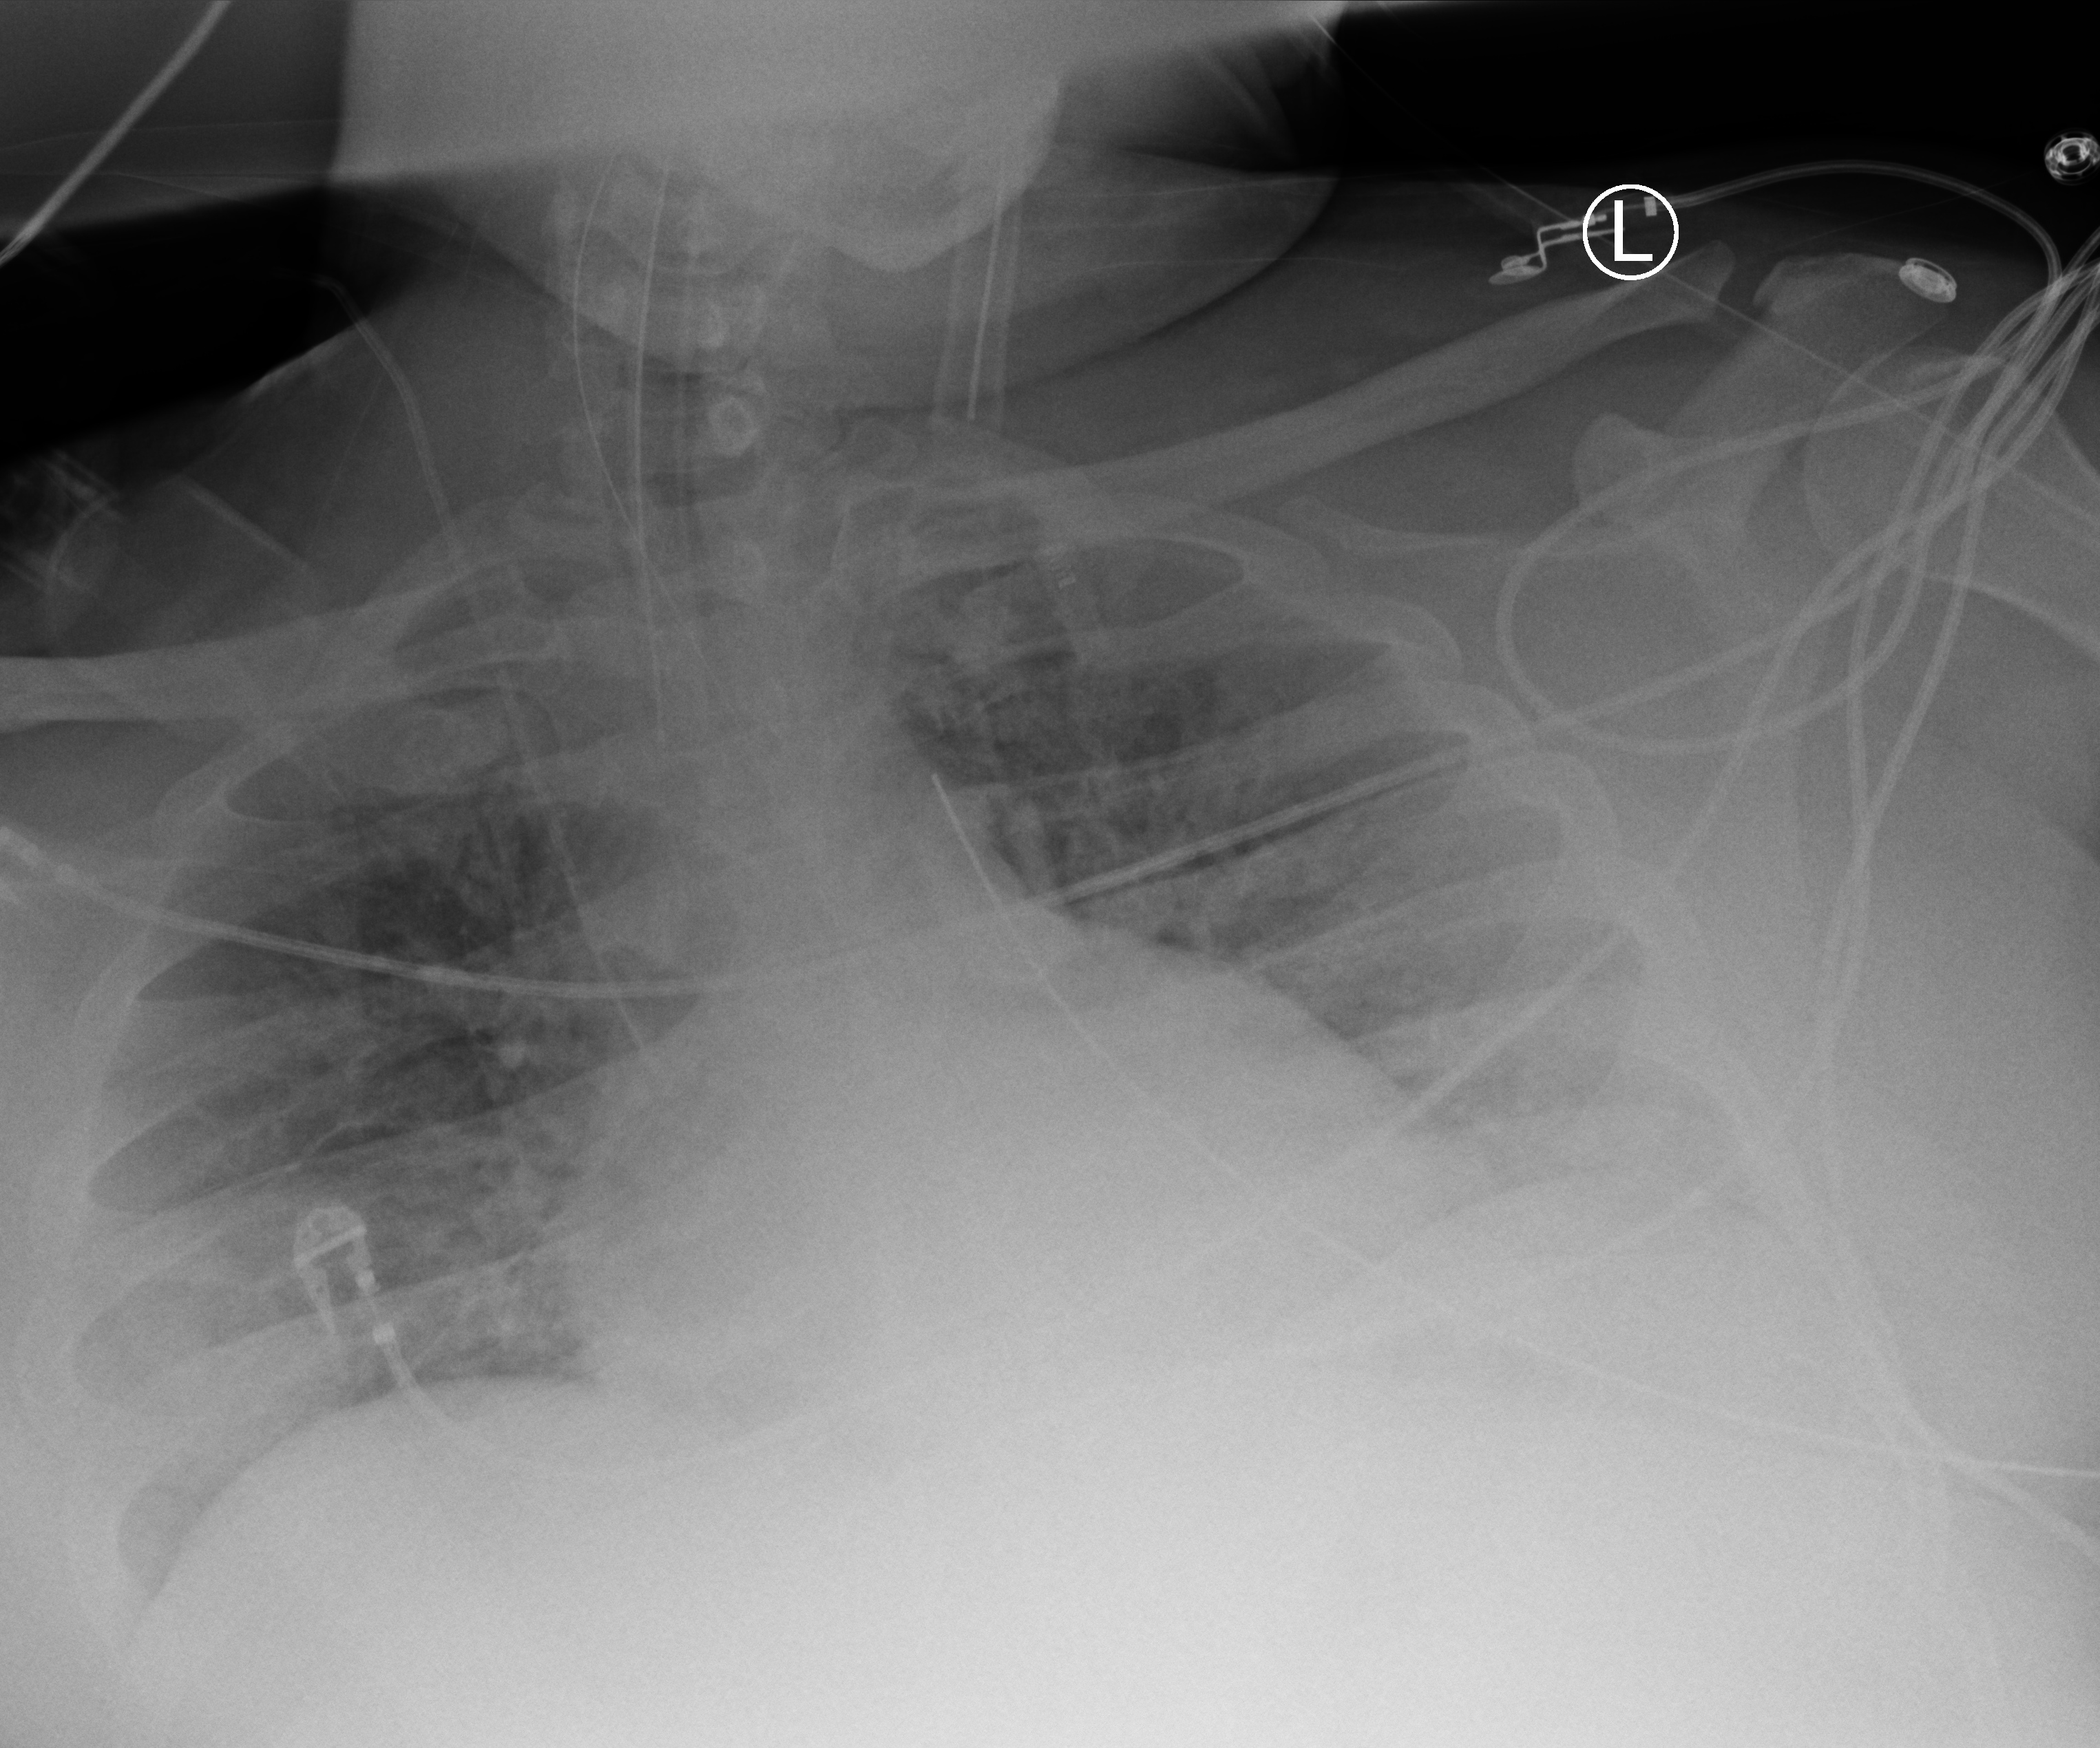
Bedside chest radiograph (computed radiography), anteroposterior (AP) projection. Patient hospitalised with COVID-19; male, aged 18–59 years.
Admission-level facts for this patient (not findings on this image; timing relative to this image not recorded): length of hospital stay: 69 days.